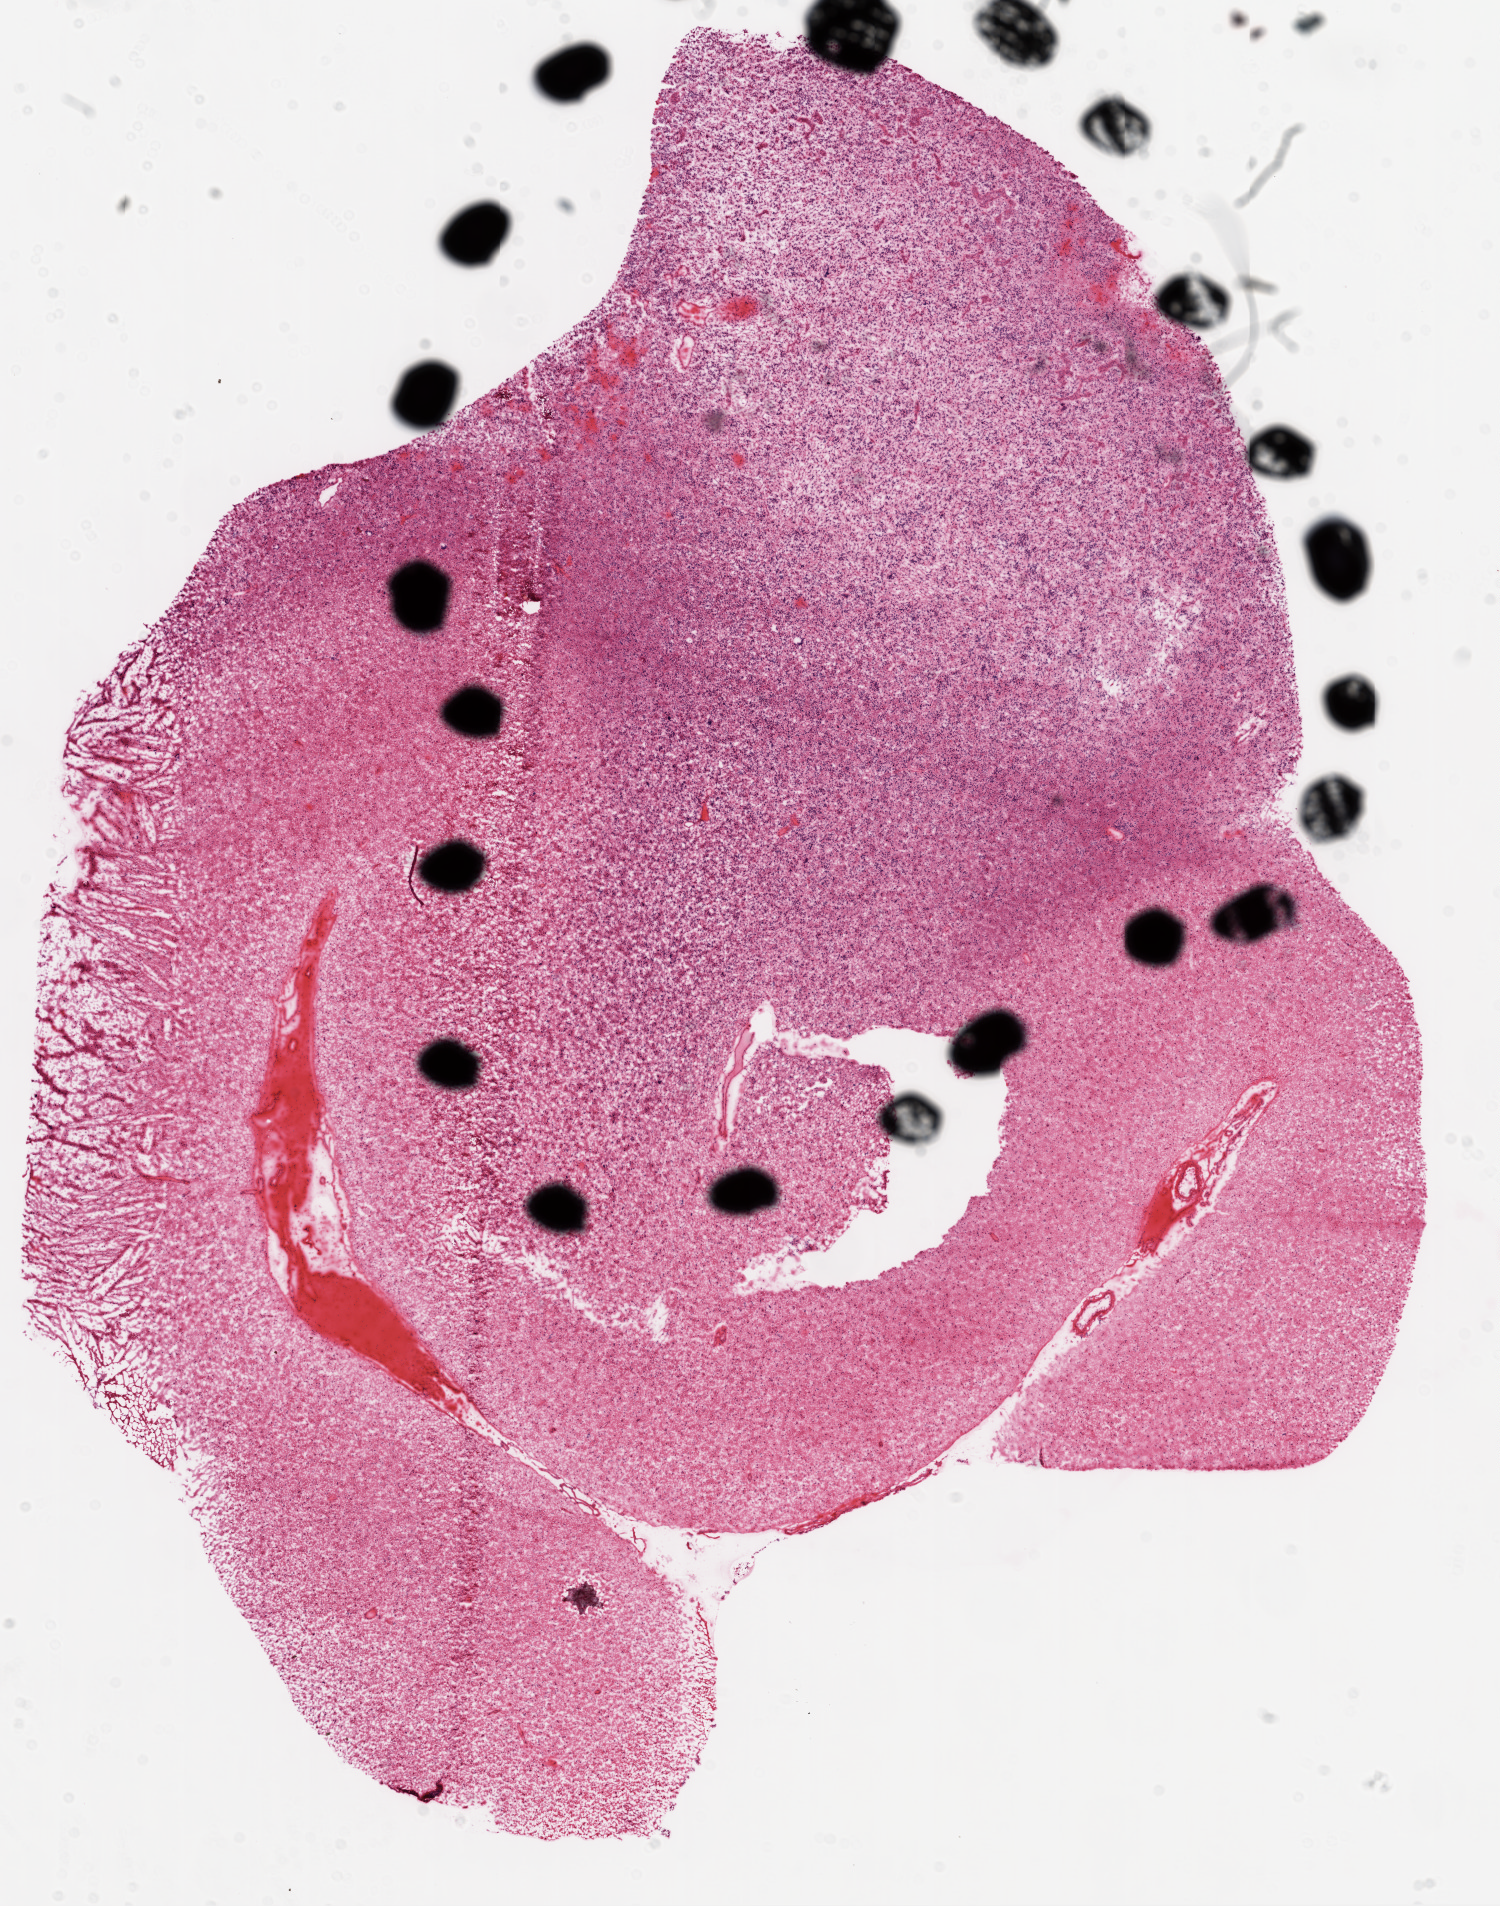
H&E whole-slide image — shown as a low-resolution overview of the whole scanned area (about 12.0 x 15.3 mm, acquisition: 20x scan); frozen section; primary tumour sample from the brain. Male, age 65 years at initial diagnosis. Slide review estimates, as recorded: tumour cells 90%, tumour nuclei 95%, normal cells 0%, stromal cells 10%, necrosis 0%.
Diagnosis: Glioblastoma.